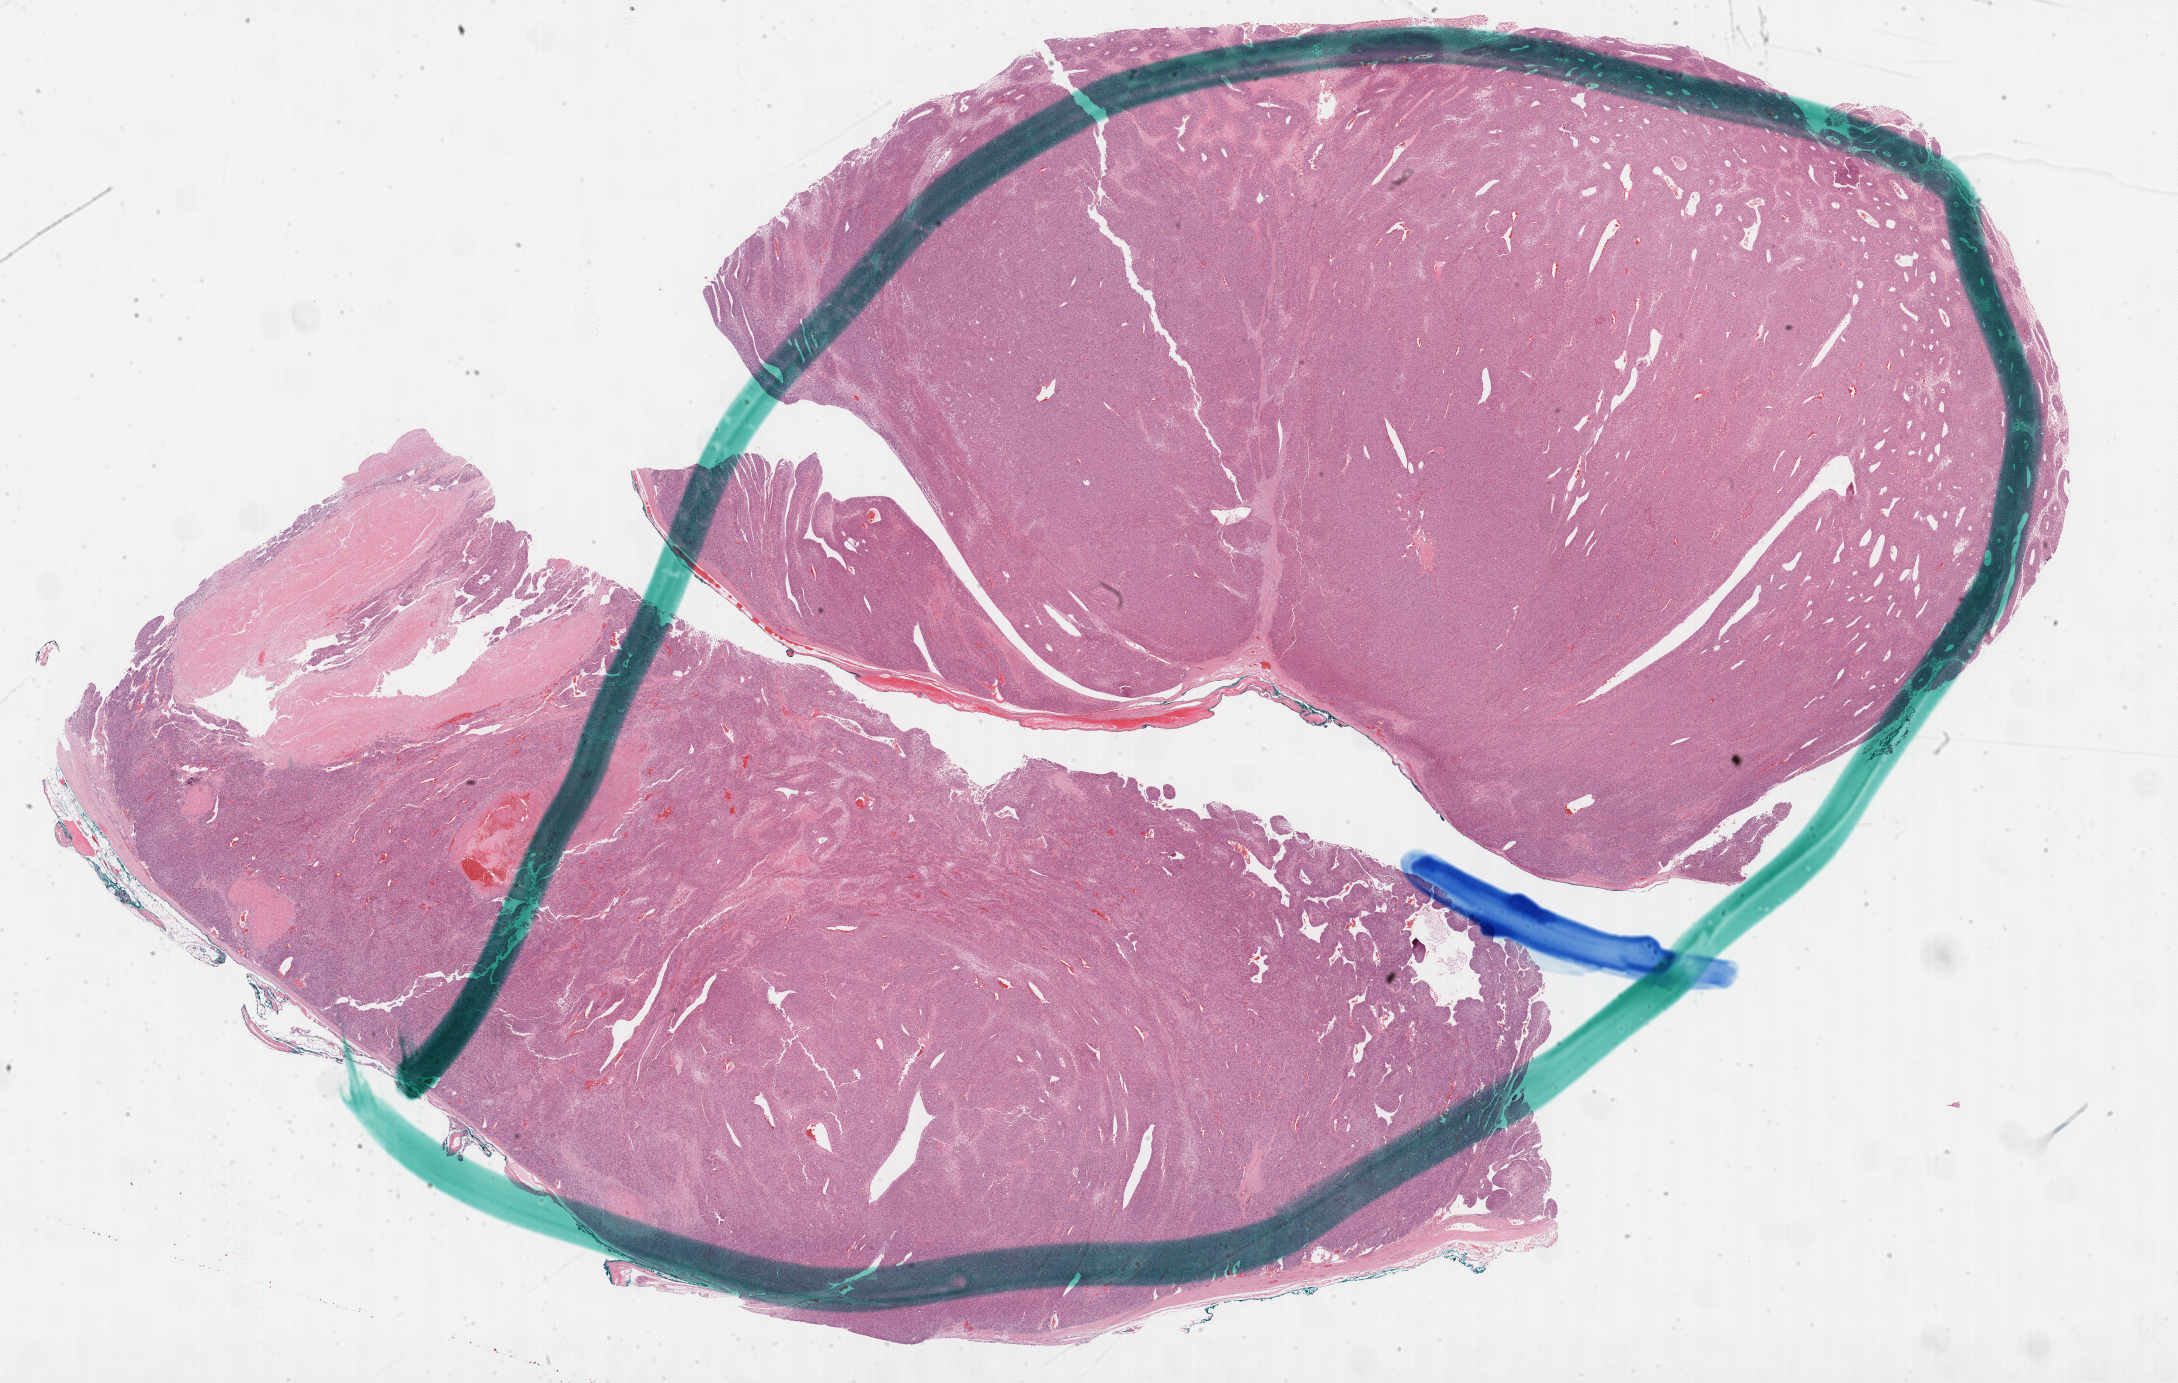
Hematoxylin and eosin (H&E) stained whole-slide image, whole scanned area (about 35.2 x 22.4 mm, from a 40x scan) shown as a low-resolution overview; formalin-fixed paraffin-embedded (FFPE) diagnostic section; primary tumour sample from the adrenal cortex. Female patient; age at initial diagnosis 59 years.
Diagnosis: Adrenal cortical carcinoma.